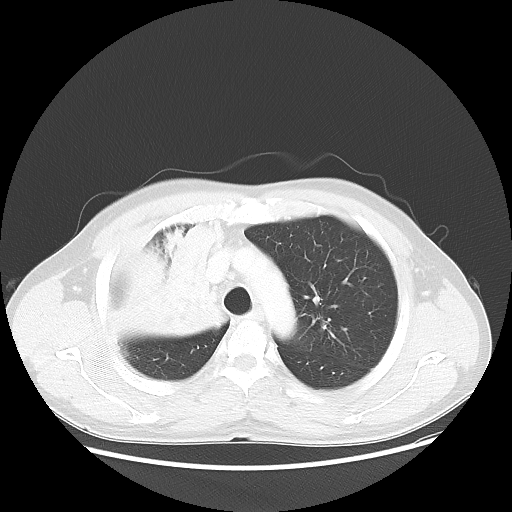
Chest CT, one axial slice; position 41 of 56 along the scan axis; 100 kVp; lung window (W 1500 / L -600 HU); 5 mm slice thickness; 512 × 512 image matrix. Male patient, age 60 years. From the clinical record (not read from this slice): clinical TNM (as recorded): T2a N1 M0.
Annotated regions visible in this slice (rectangle marked by the reading radiologist):
- lung tumour (recorded histology: squamous cell carcinoma): bounding box (x1, y1, x2, y2) in pixels: (104, 216, 225, 354)